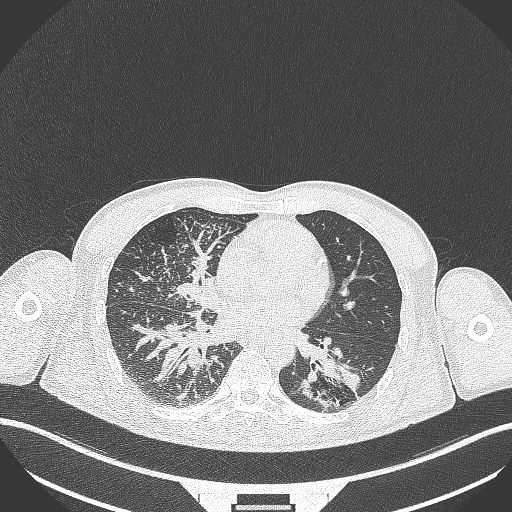
Chest CT, one axial slice. Position 142 of 348 along the scan axis. Reconstruction kernel B70f. 120 kVp. Lung window (W 1500 / L -600 HU). 1 mm slice thickness. 512 × 512 image matrix, field of view 400 × 400 mm. Male patient, age 49 years. From the clinical record (not read from this slice): clinical TNM (as recorded): T2b N1 M0.
Outlined on this slice (rectangle marked by the reading radiologist):
- lung tumour (recorded histology: adenocarcinoma): box from (x=298, y=351) to (x=366, y=410) px